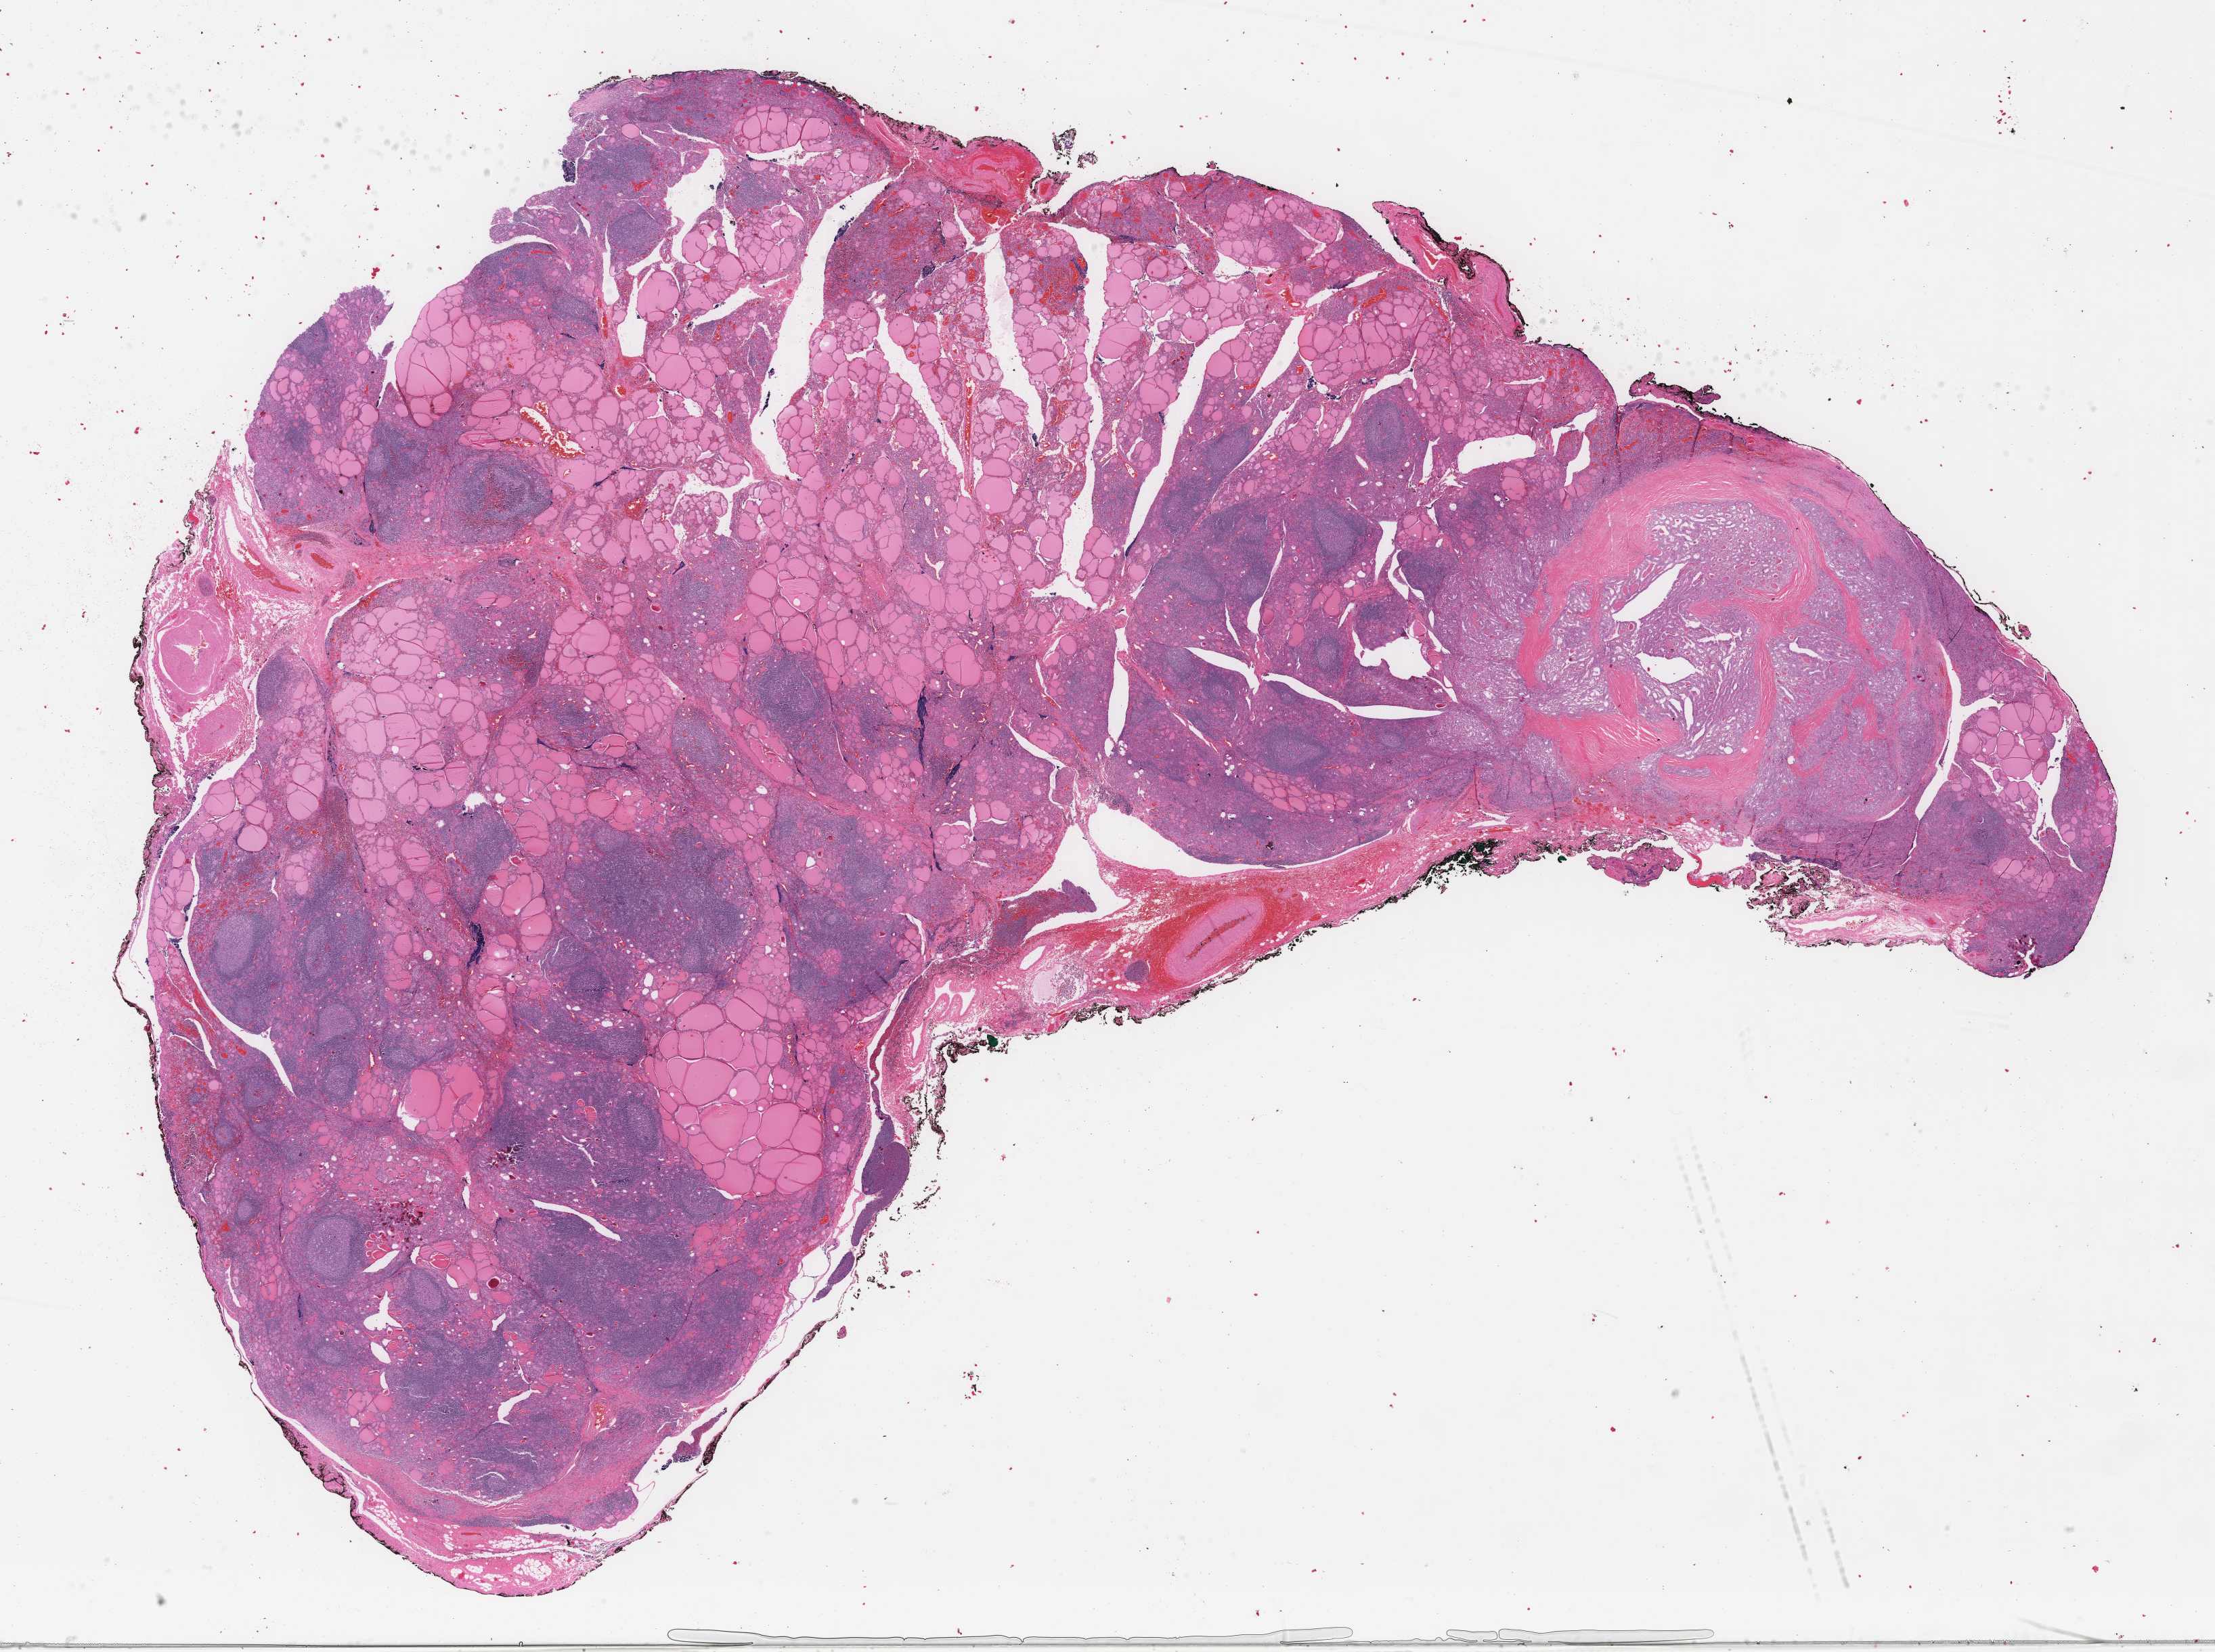
Digitized H&E tissue section (whole slide) — a low-resolution overview of the entire scanned area, about 26.0 x 19.4 mm (slide scanned at 40x); FFPE section; sample: primary tumour, thyroid. Patient: female, age at initial diagnosis 24 years.
AJCC pathologic stage: I (6th edition). Diagnosis: Papillary adenocarcinoma, NOS (thyroid gland). Lymph nodes positive (case pathology): 0 of 18 examined. Laterality: right.